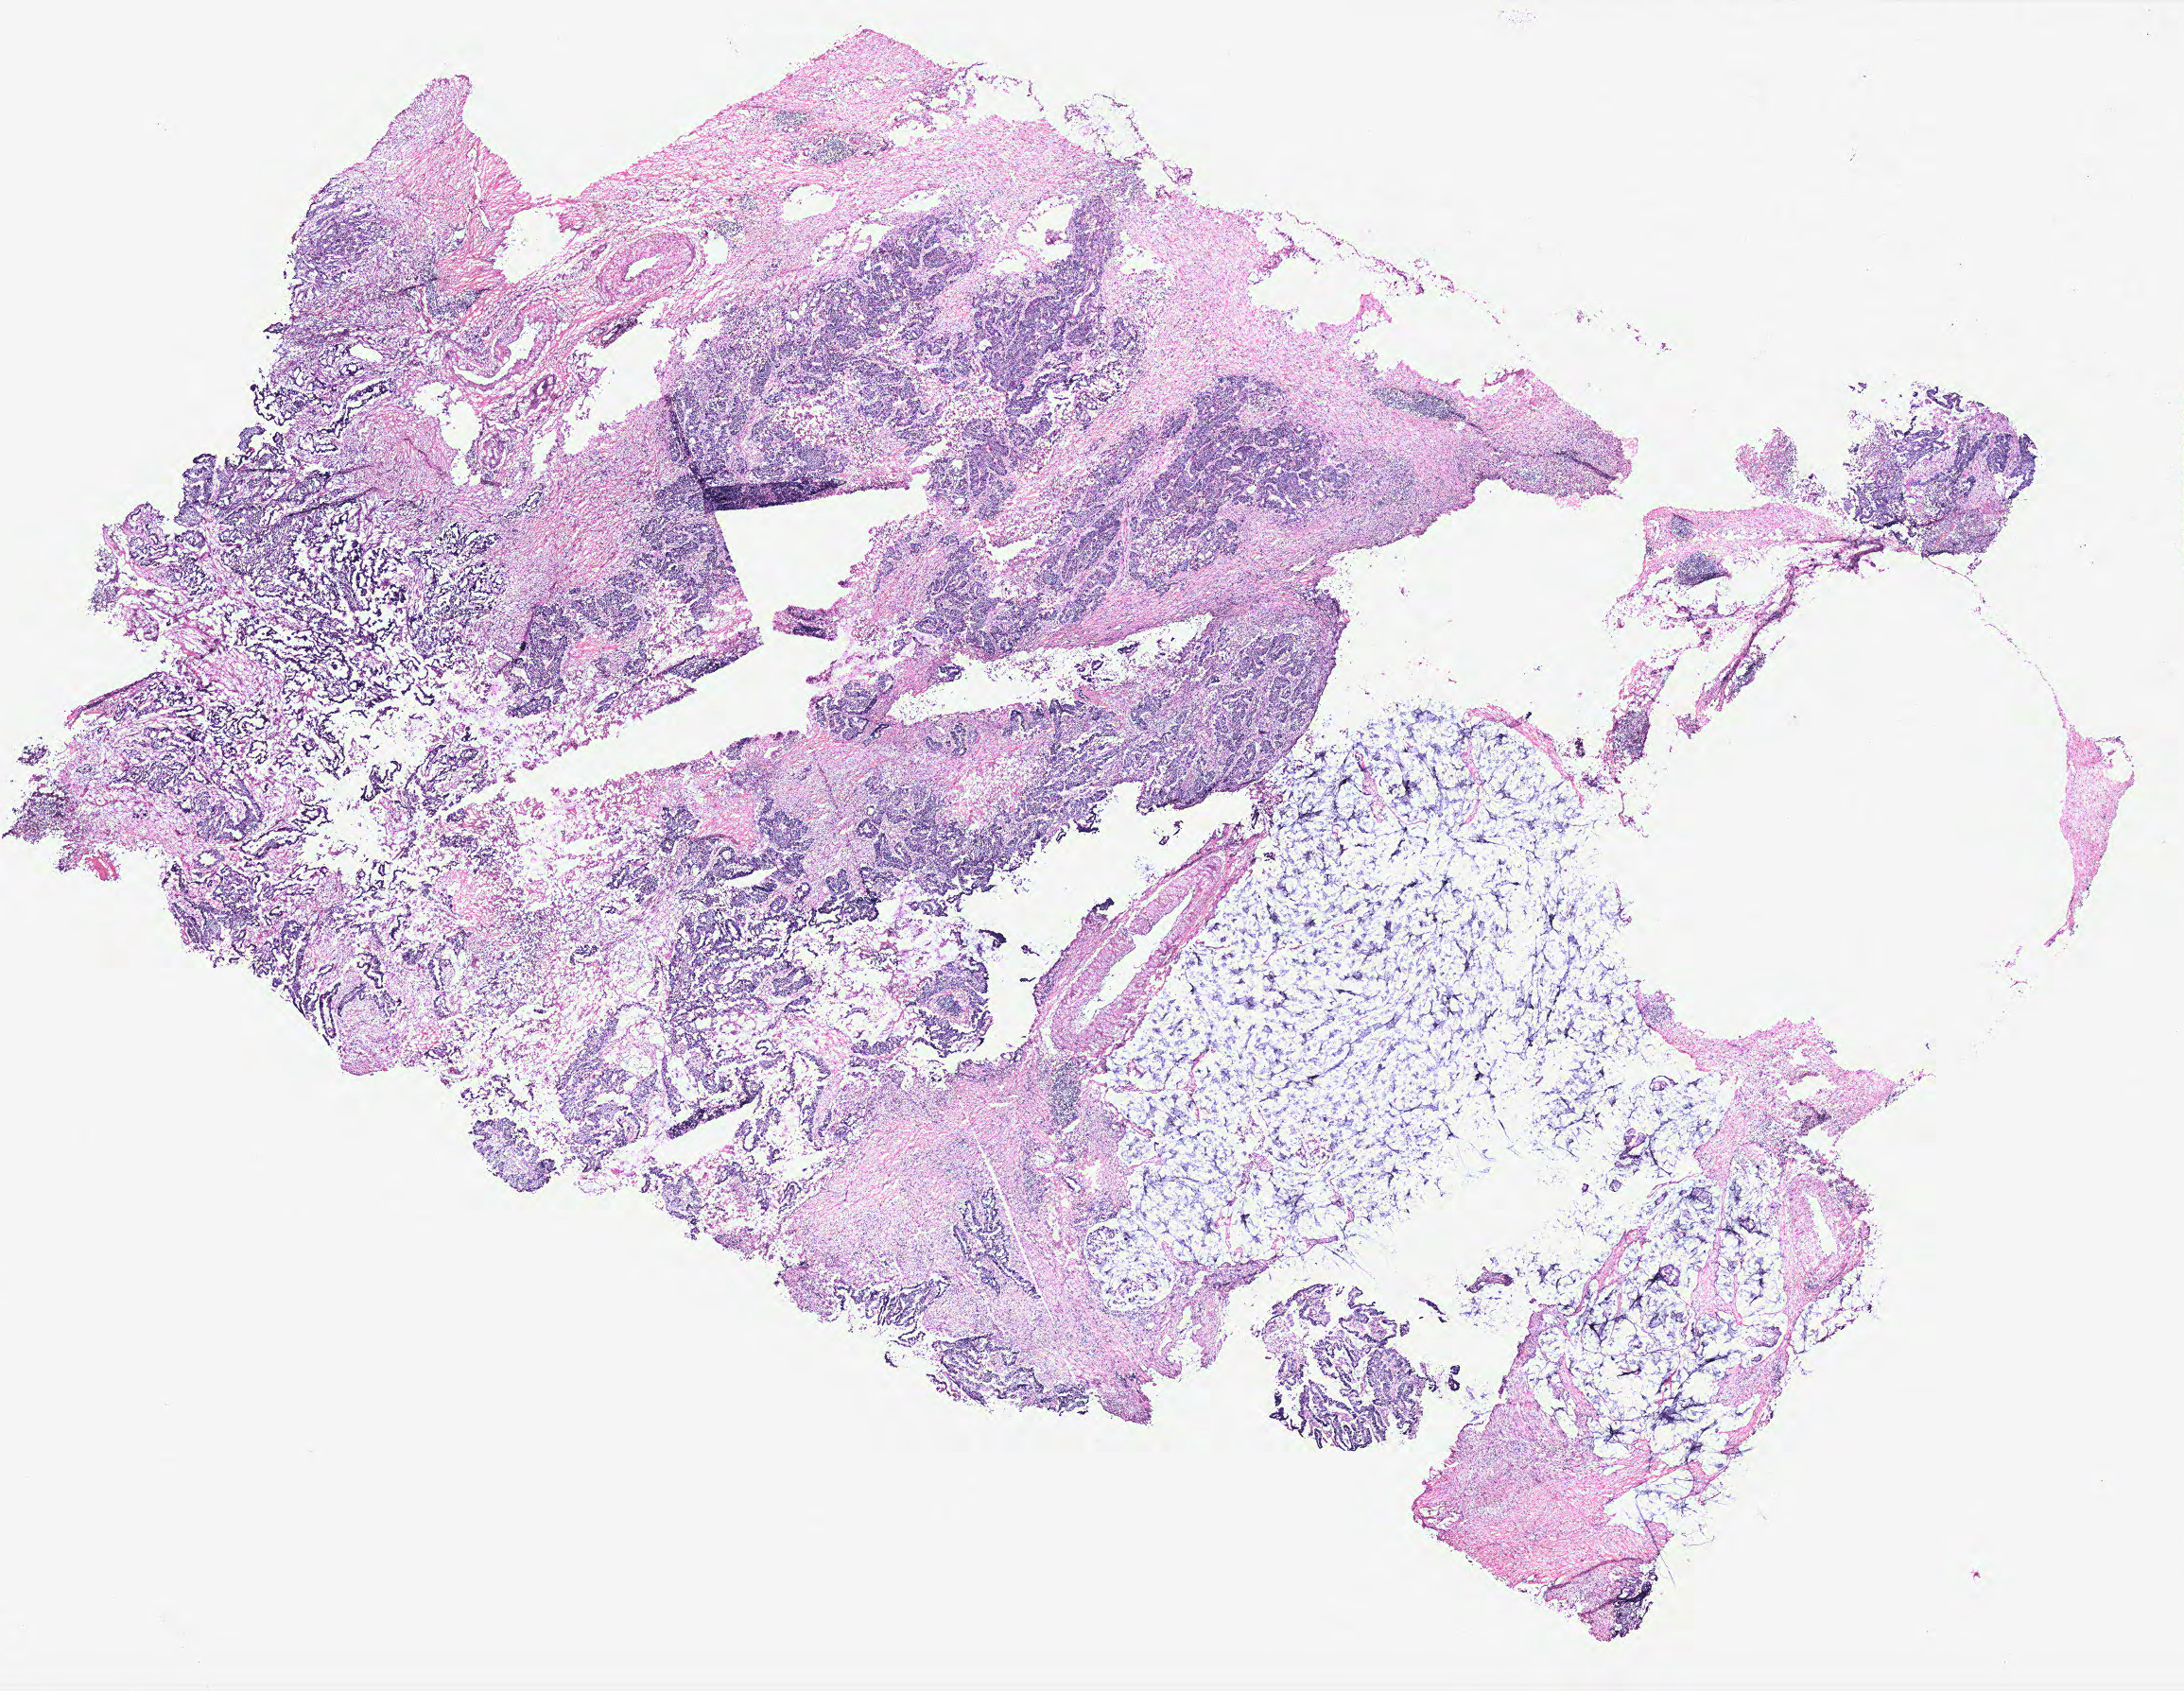
Digitized H&E tissue section (whole slide), low-resolution overview of the scanned area, about 18.5 x 14.3 mm. Colon, tumour tissue. Male, 35 y/o.
Histologic diagnosis: Adenocarcinoma, NOS. Primary tumour site (as recorded): colon. AJCC pathologic stage: IIIB.